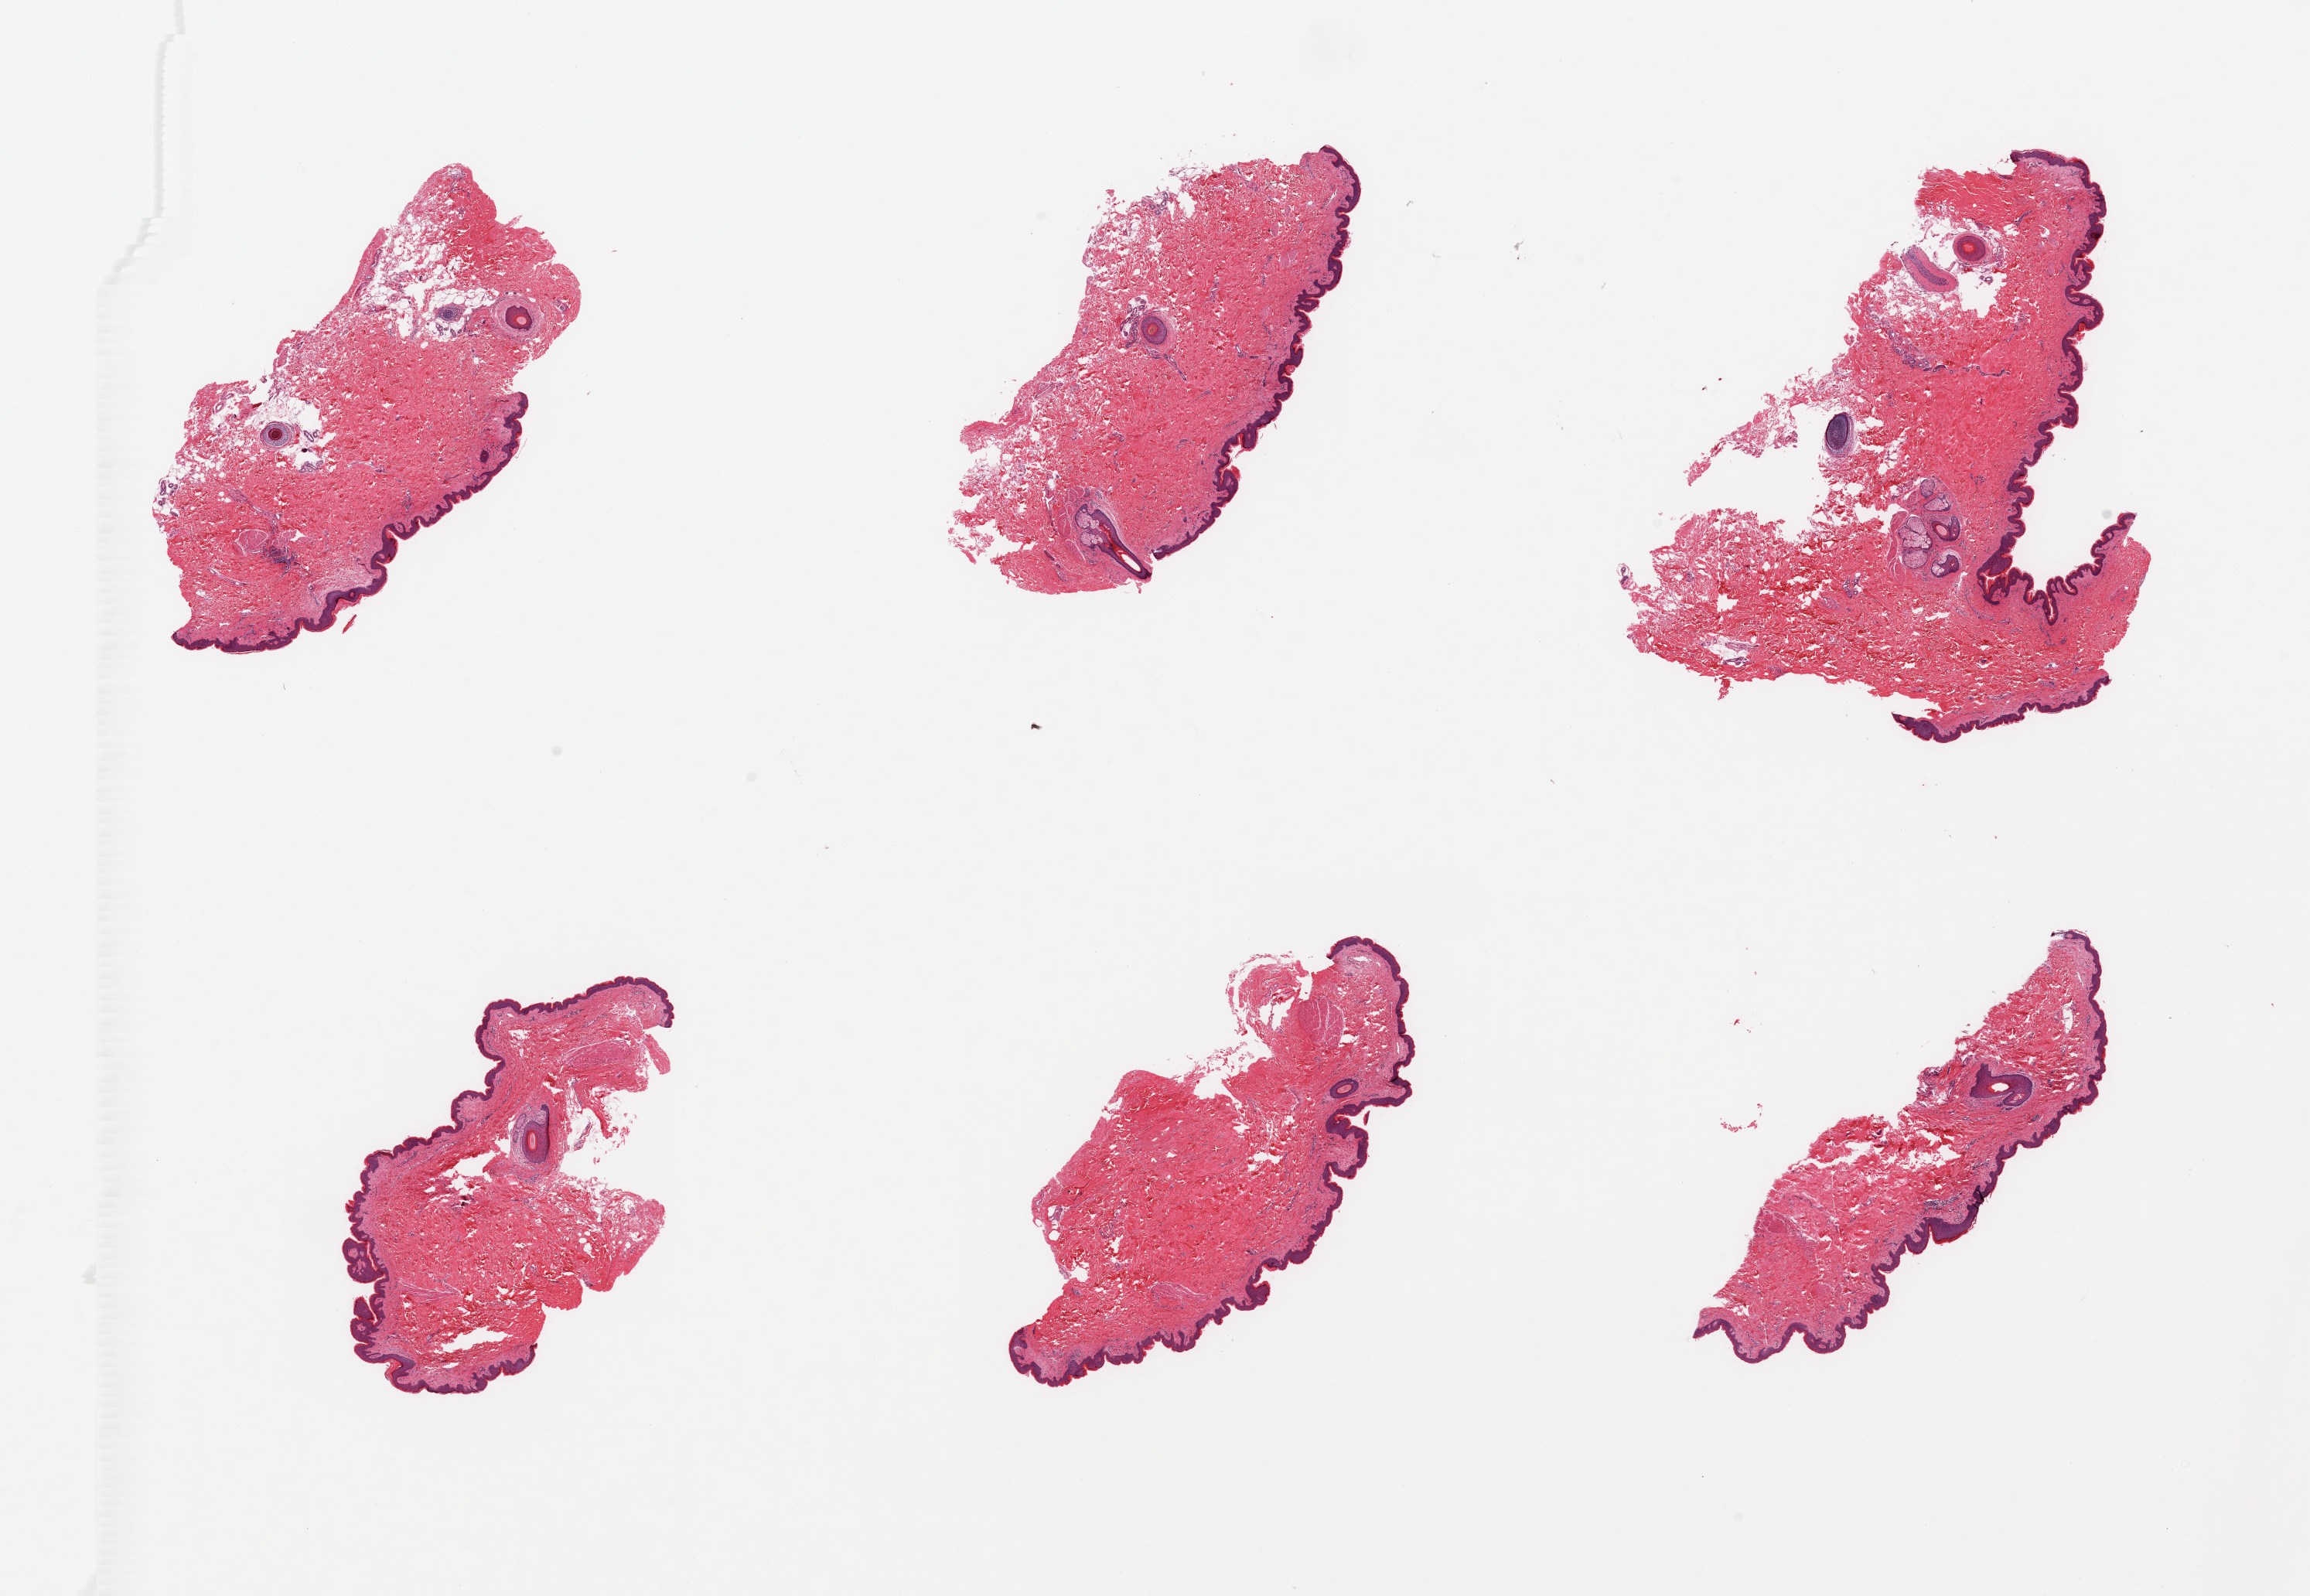
H&E whole-slide image — low-resolution overview of the scanned area, about 23.6 x 16.3 mm (from a 20x scan); PAXgene-fixed paraffin-embedded (PFPE) section; target tissue: skin of suprapubic region; tissue donor sample. Donor sex: female.
Review note (as recorded): 6 pieces, trace dermal fat; squamous epithelium is ~35-45 microns.